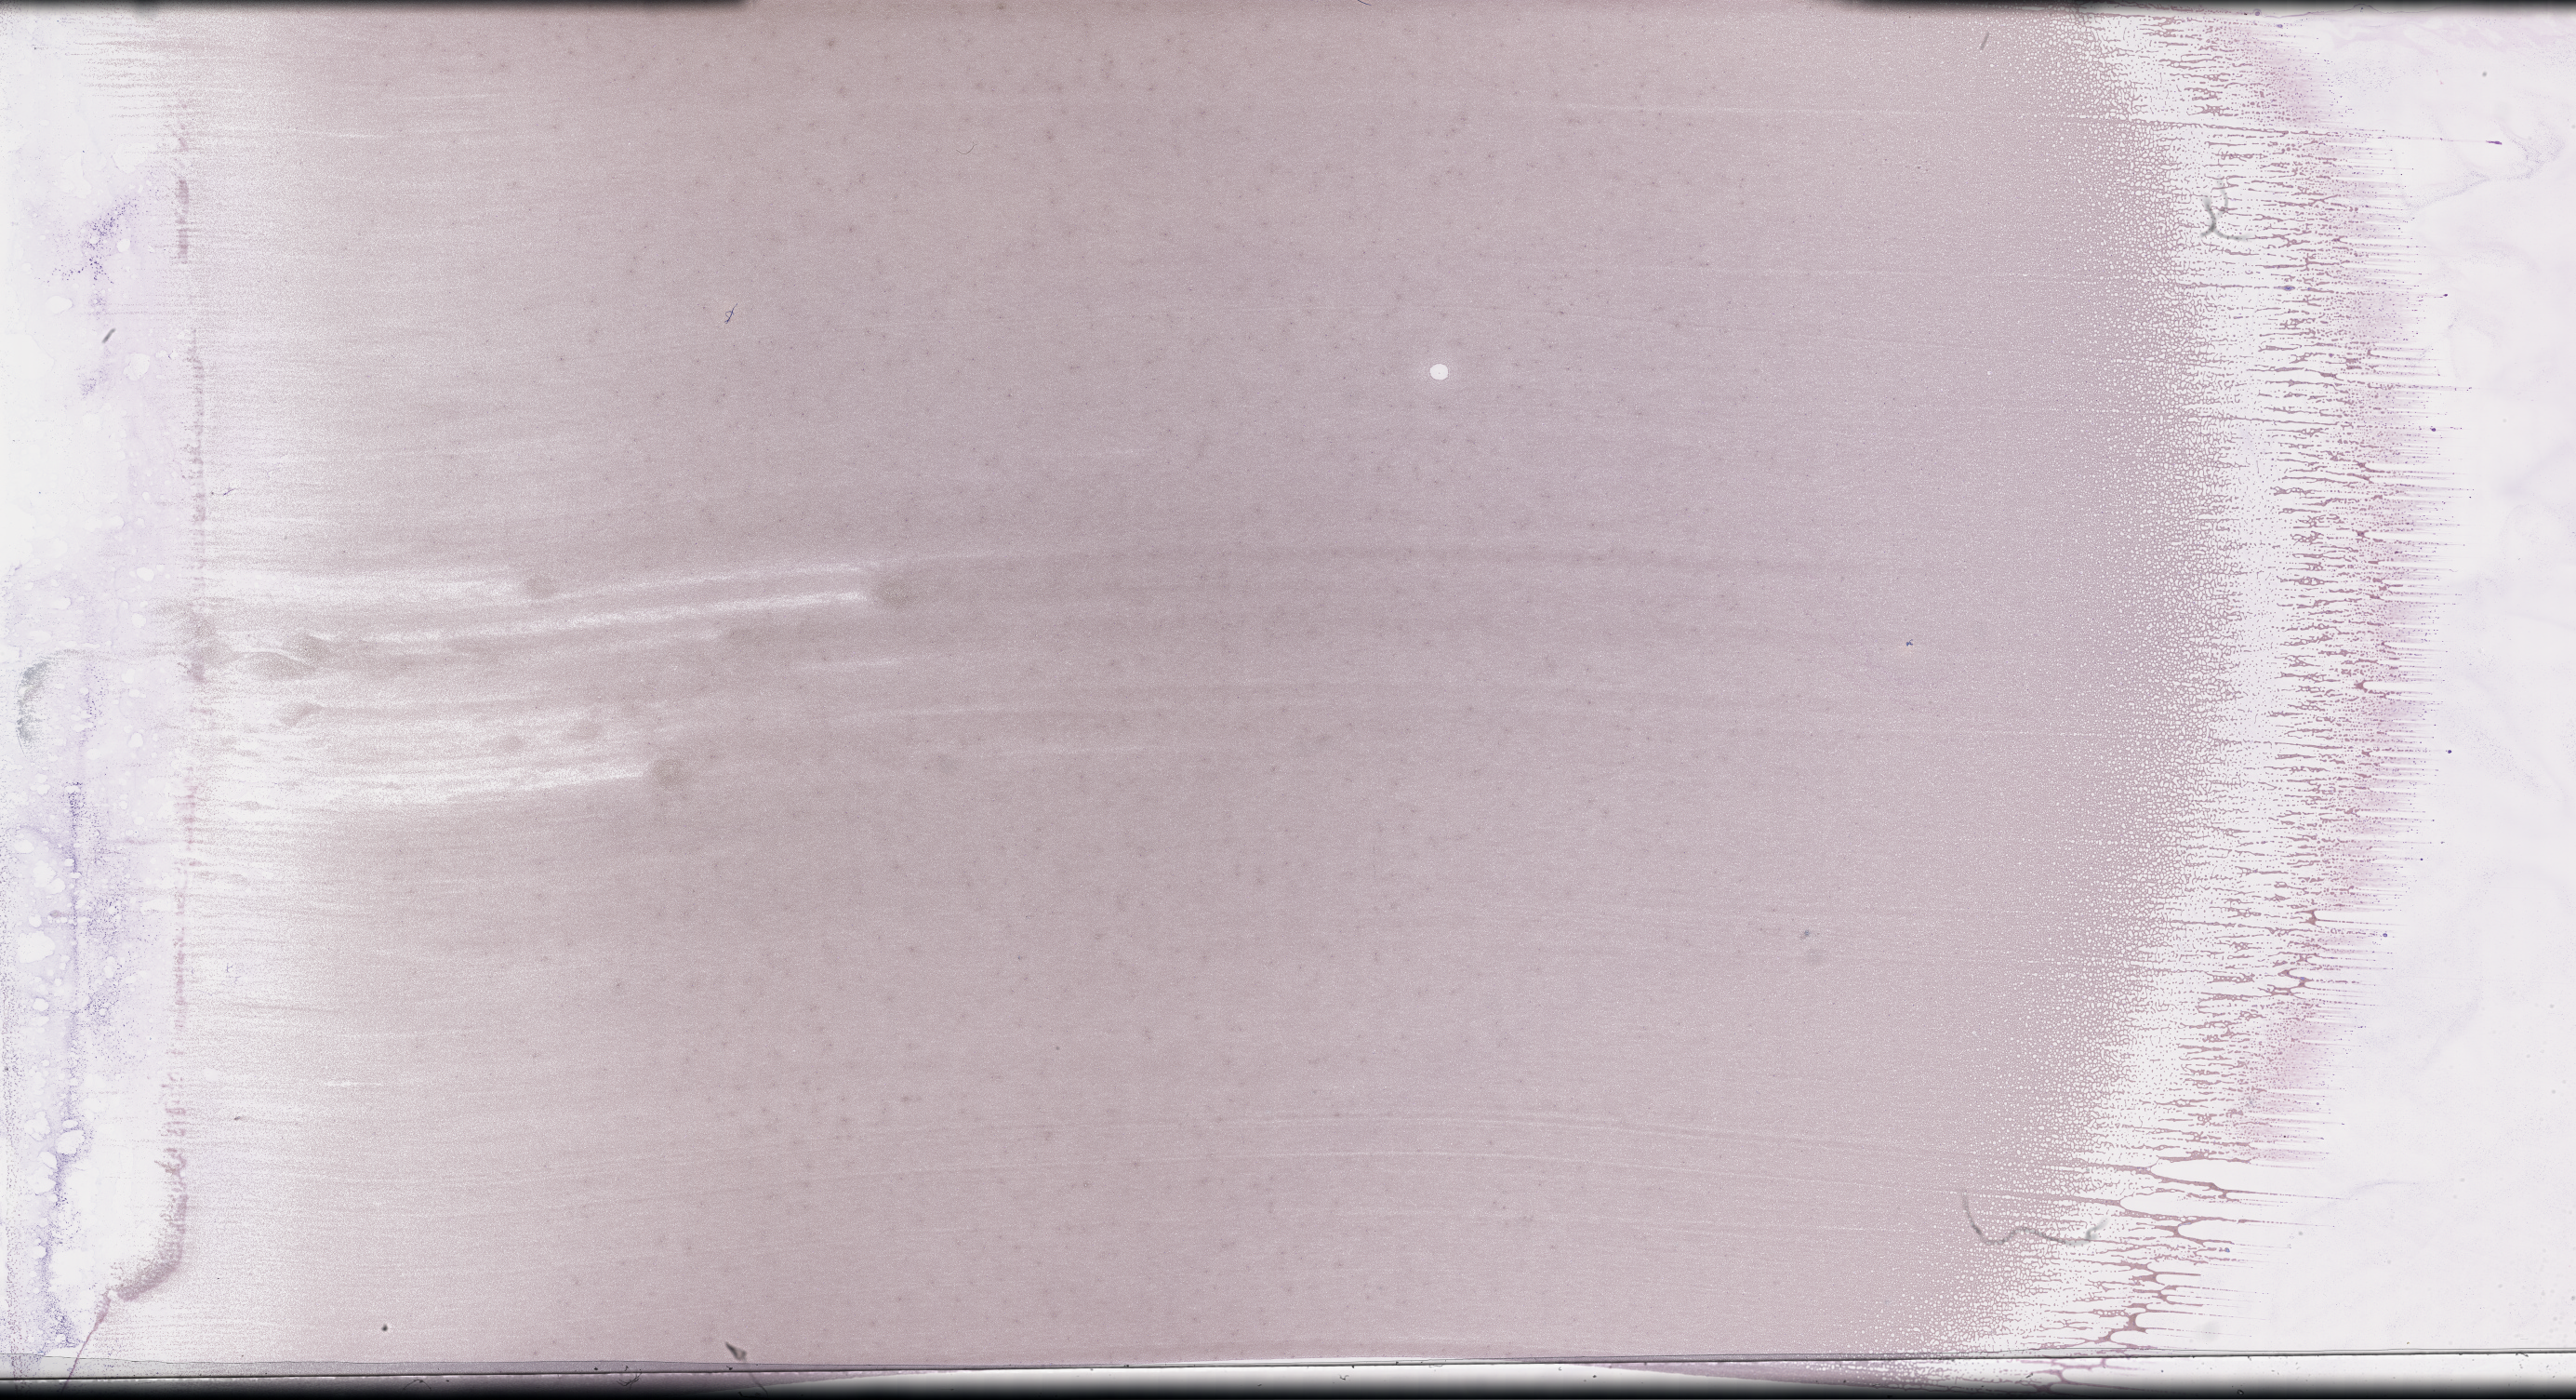
Wright–Giemsa-stained whole blood smear, whole-slide image — shown as a low-resolution overview of the whole scanned area (about 44.7 x 24.3 mm), smear from an EDTA sample. Patient: male.
* patient diagnosis: Plasma Cell Myeloma